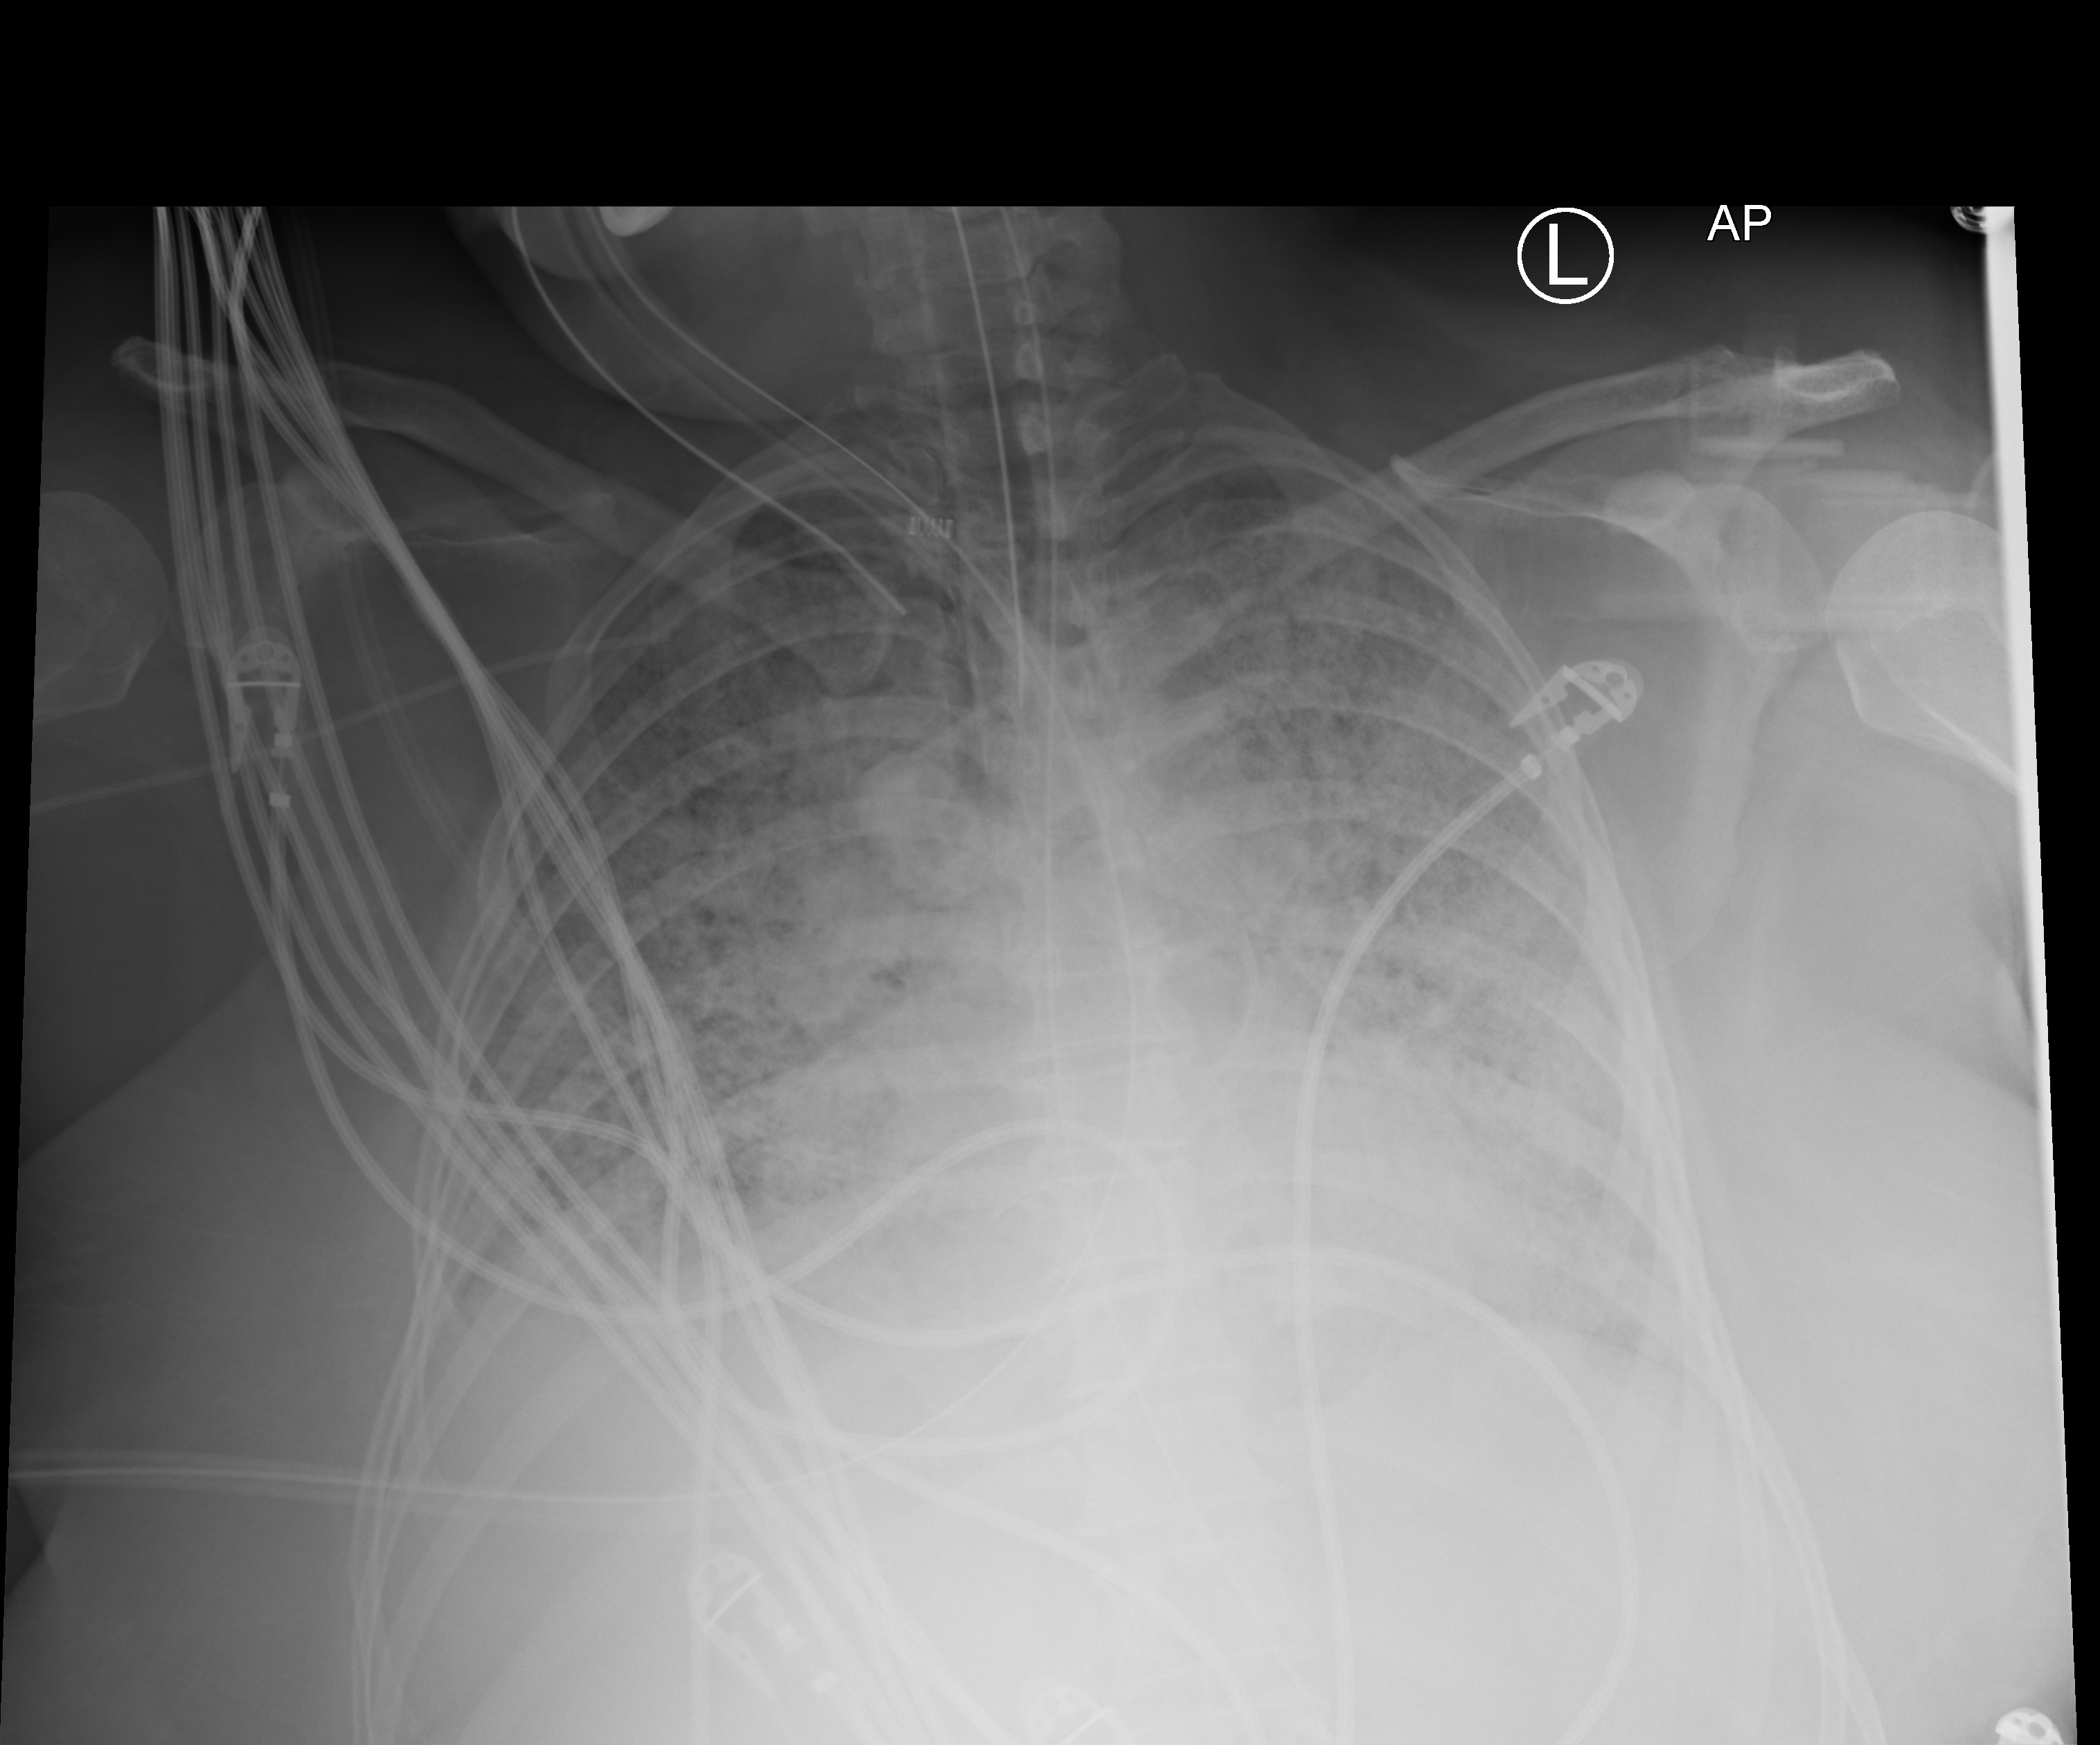
Chest X-ray (portable); anteroposterior (AP) projection. Patient hospitalised with COVID-19; female, aged 18–59 years.
Admission-level facts for this patient (not findings on this image; timing relative to this image not recorded): other chronic lung disease (admission record): no.